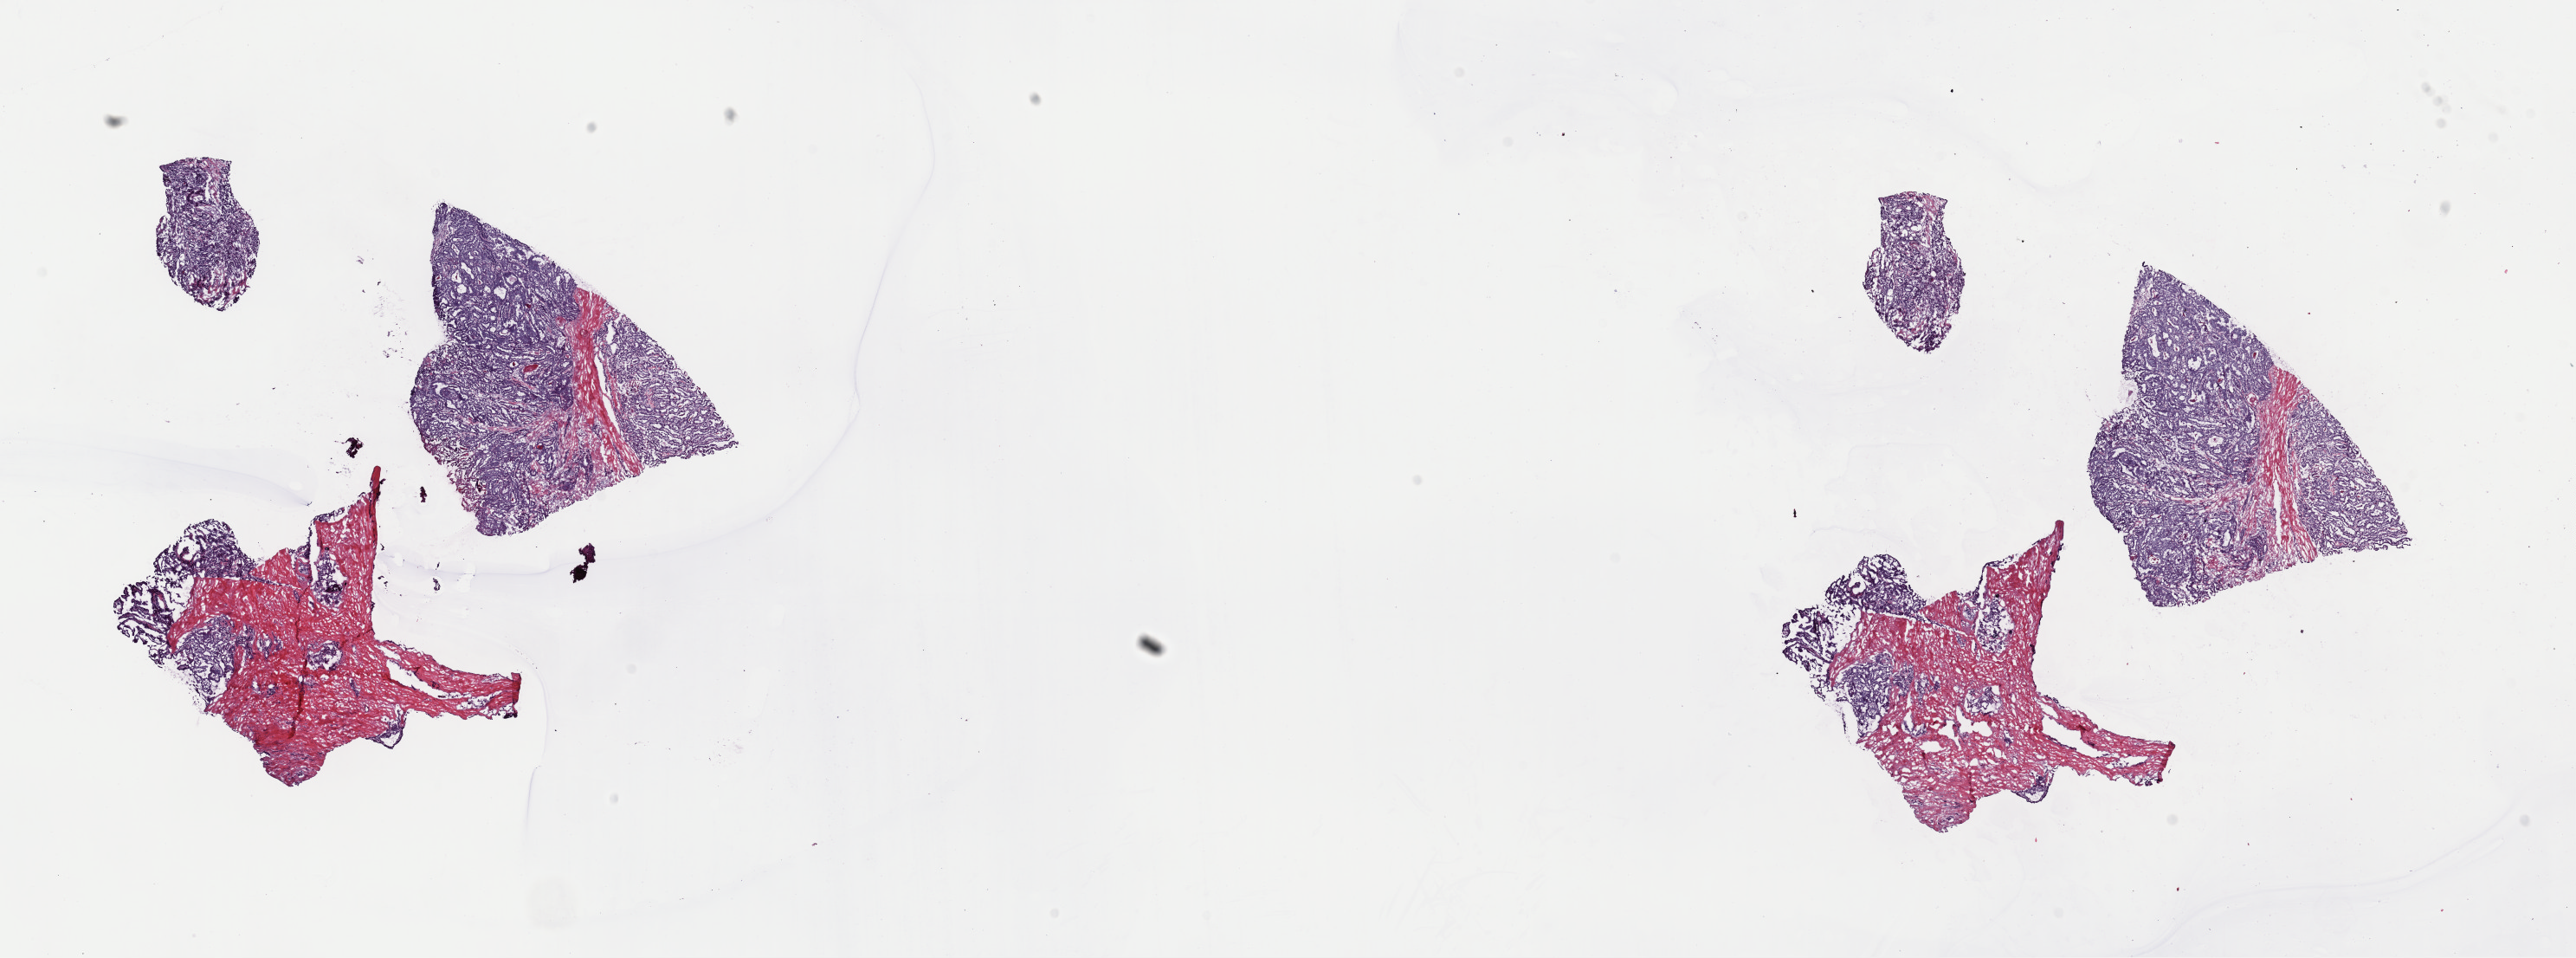
Digitized Hematoxylin and eosin (H&E) stained tissue section (whole slide) — whole scanned area (about 23.5 x 8.7 mm) shown as a low-resolution overview; frozen section; sample: primary tumour, thyroid. Female, age 40 years at initial diagnosis. Pathologist review of this section (percent, as recorded): tumour cells 60%, tumour nuclei 75%, normal cells 0%, stromal cells 40%, necrosis 0%. Inflammatory infiltration, as recorded: lymphocyte infiltration 4%, monocyte infiltration 2%, neutrophil infiltration 0%.
Diagnosis: Papillary adenocarcinoma, NOS (thyroid gland). AJCC pathologic stage: I.